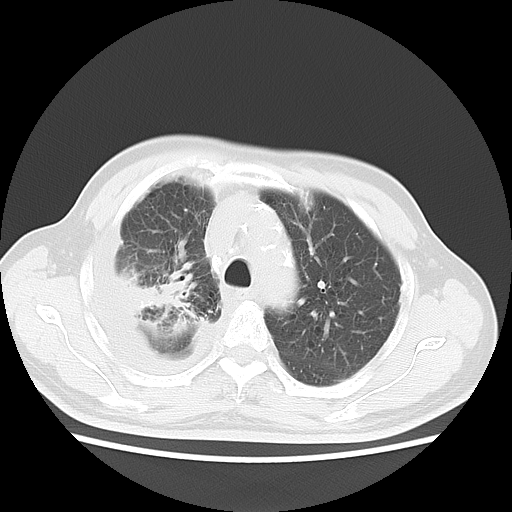
Chest CT, one axial slice; slice 11 of 16 in the series (ordered by position); reconstruction kernel LUNG; lung window (W 1500 / L -600 HU); 512 × 512 image matrix. Male patient, age 75 years. Case-level facts recorded for this patient, not image findings: clinical TNM (as recorded): T1c N1 M1.
Annotated regions visible in this slice (bounding box drawn by a radiologist):
- lung tumour (recorded histology: adenocarcinoma): box from (x=117, y=268) to (x=187, y=318) px